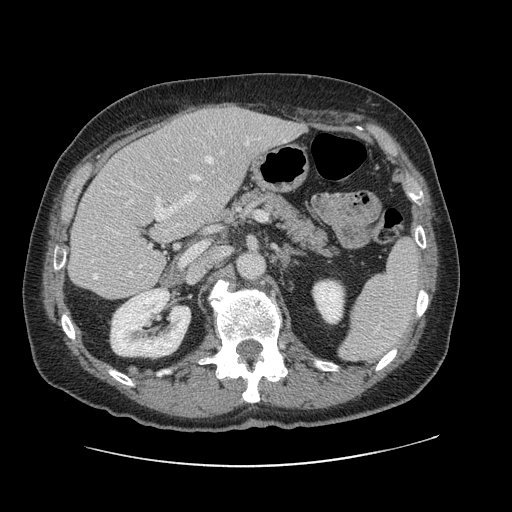
Contrast-enhanced abdominal CT, one axial slice; slice 60 of 138 in the series (ordered by position); 120 kVp; soft-tissue window (W 400 / L 40 HU); 2.5 mm slice thickness; 512 × 512 image matrix, field of view 402 × 402 mm. Male patient, age 71 years. Case-level facts recorded for this patient, not image findings: diagnosis: colorectal cancer liver metastases, imaged before liver resection; multiple liver metastases: no; largest metastasis: 3.3 cm; disease in both lobes: no.
Structures marked on this image (expert manual segmentation):
- hepatic veins: bounding box [x1, y1, x2, y2] px = [93, 156, 227, 280]
- liver: [71, 105, 303, 299]
- planned liver remnant (the part of the liver to remain after resection): [71, 144, 203, 299]
- portal vein (with intrahepatic branches): [96, 140, 249, 250]